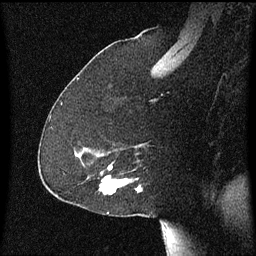
Breast MRI (dynamic contrast-enhanced), one sagittal slice; position 37 of 60 along the scan axis; dynamic contrast-enhanced series, image 2 of 3 at this slice position (ordered by acquisition); 1.5 T; TE 4.2 ms, TR 8.4 ms; 2 mm slice thickness; 256 × 256 image matrix, field of view 200 × 200 mm. Female patient, age 59 years.
Outlined on this slice (semi-automatically segmented with operator editing):
- analysis volume of interest (the breast-tissue region the enhancement analysis was run in; not a lesion): box from (x=98, y=166) to (x=143, y=195) px
- tumour enhancement mask (voxels above the 70 % enhancement threshold inside the analysis volume of interest): (x=102, y=176)–(x=139, y=189)